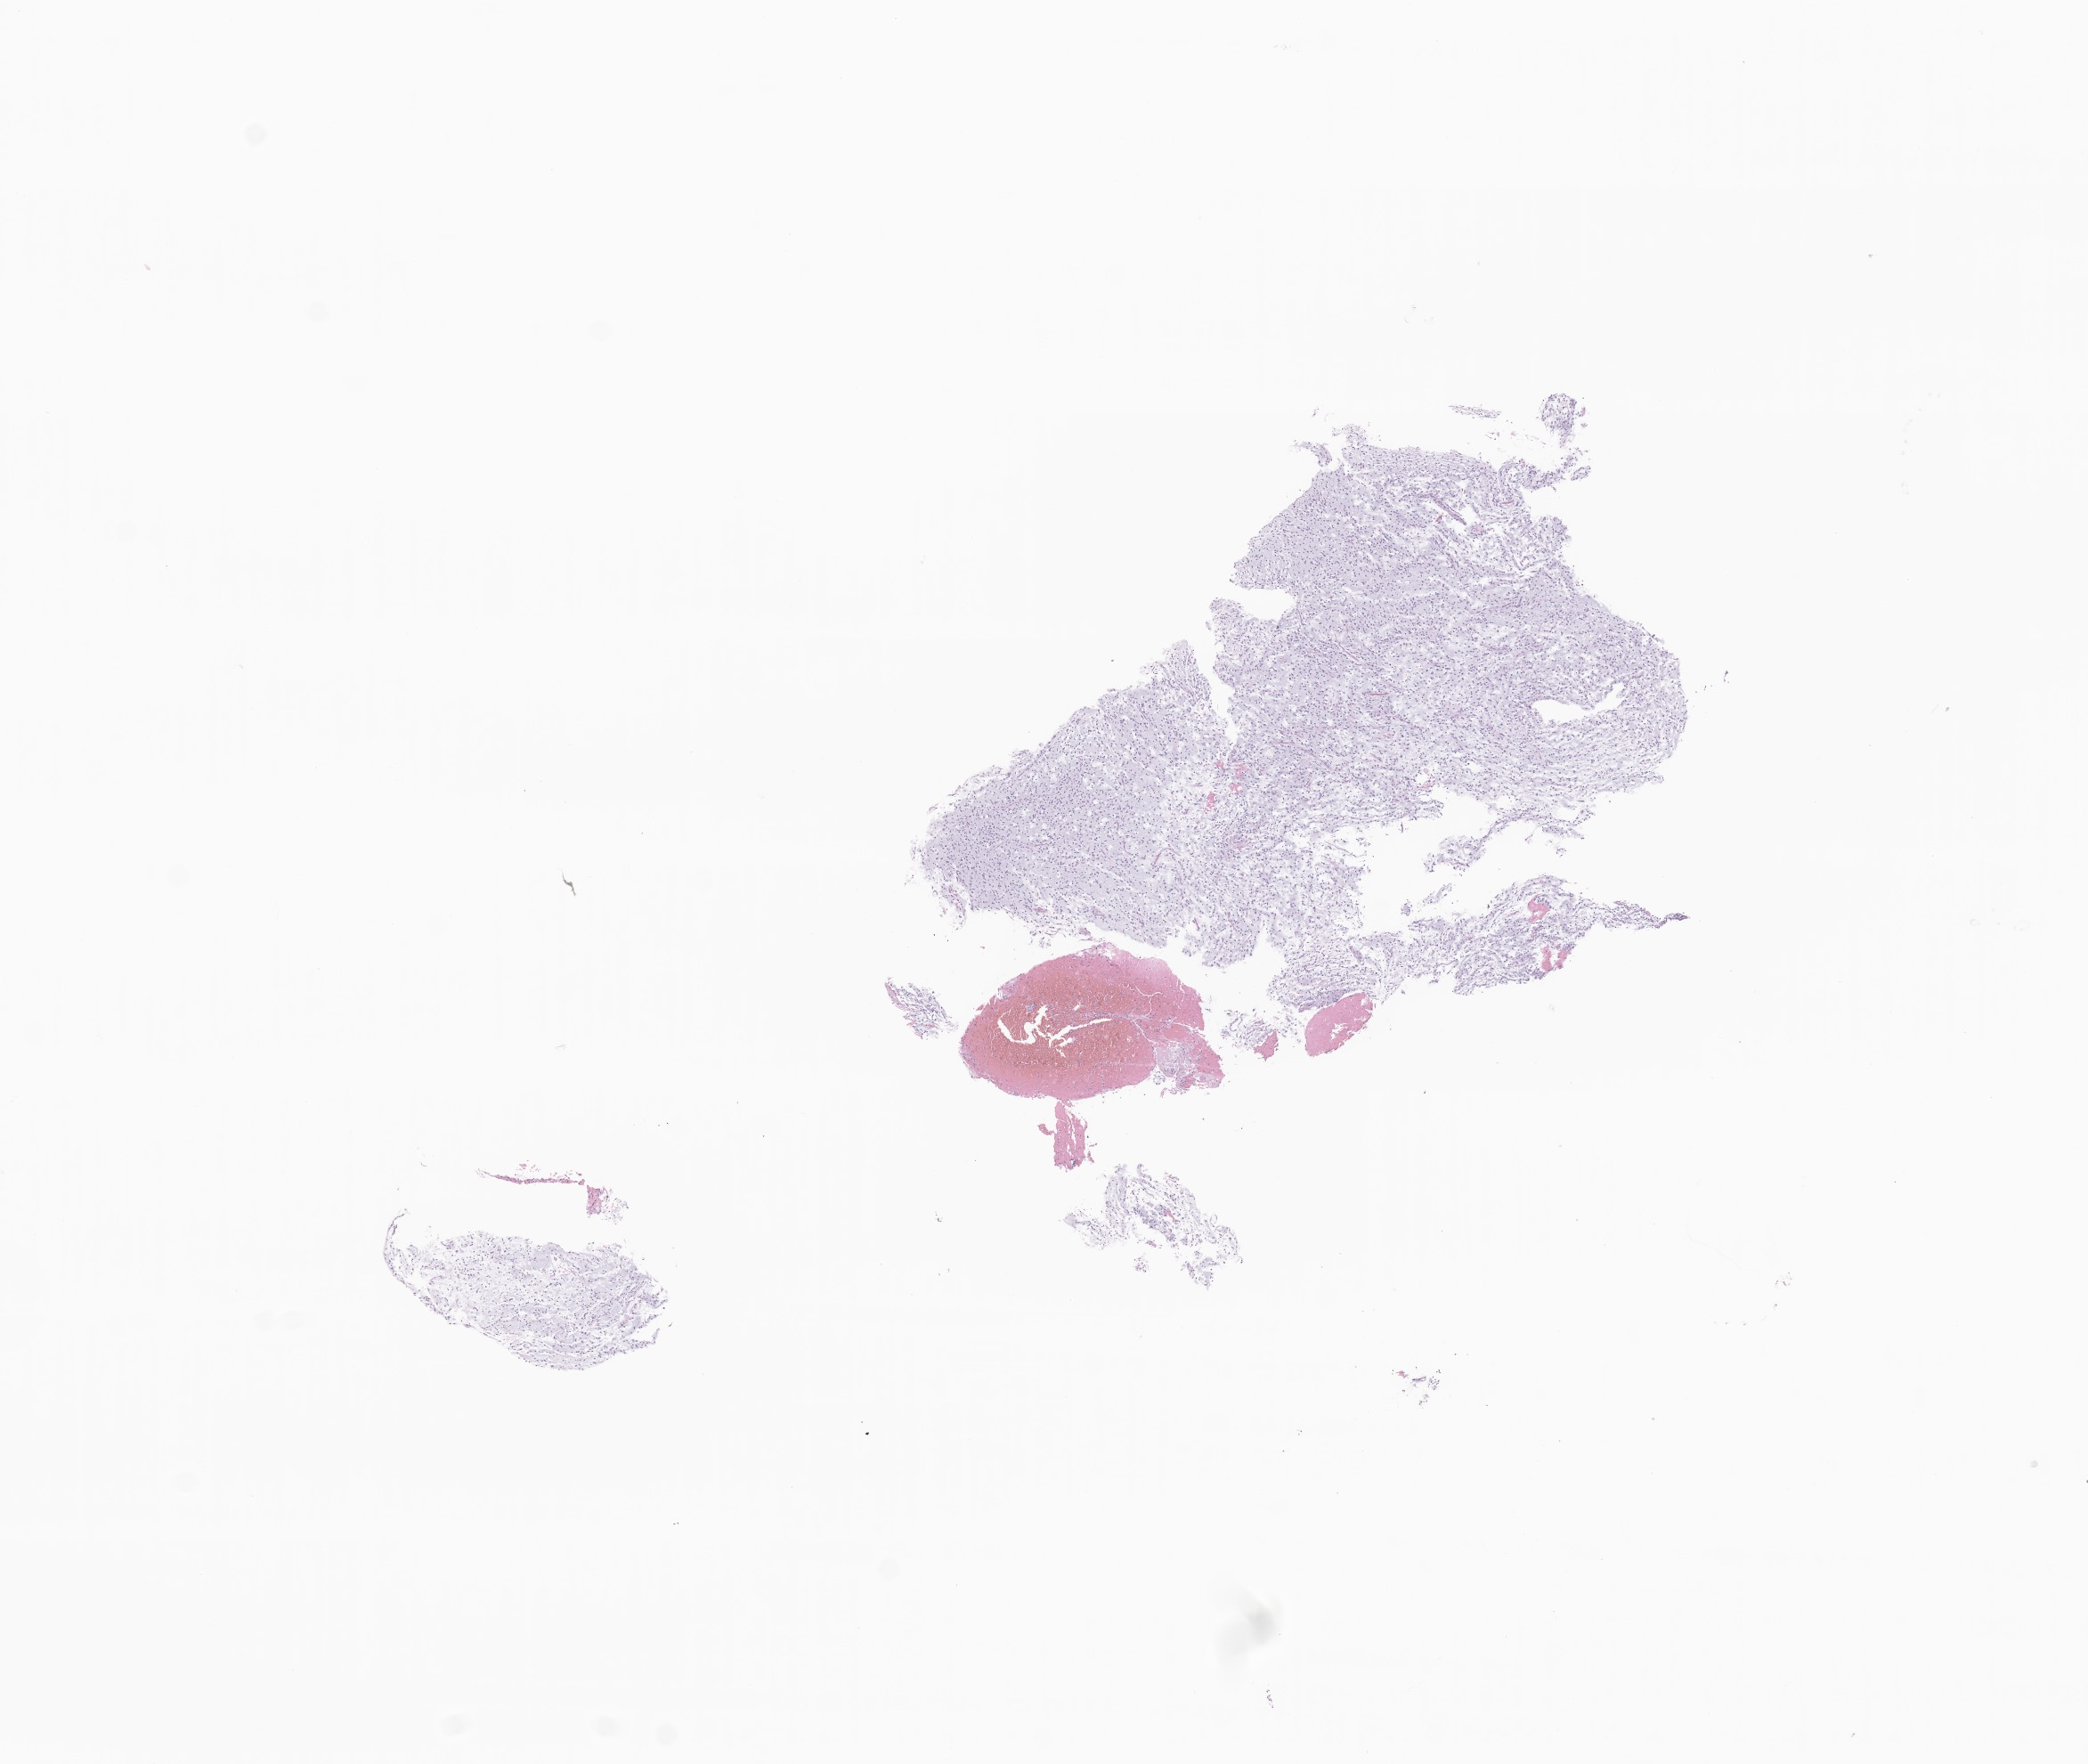
H&E whole-slide image of tumor tissue from the brain, low-resolution overview of the scanned area, about 9.9 x 8.4 mm. Formalin-fixed, paraffin-embedded (FFPE) tissue. Patient: female, age 712 days (about 1.9 years).
Diagnosis: Astrocytoma, NOS.